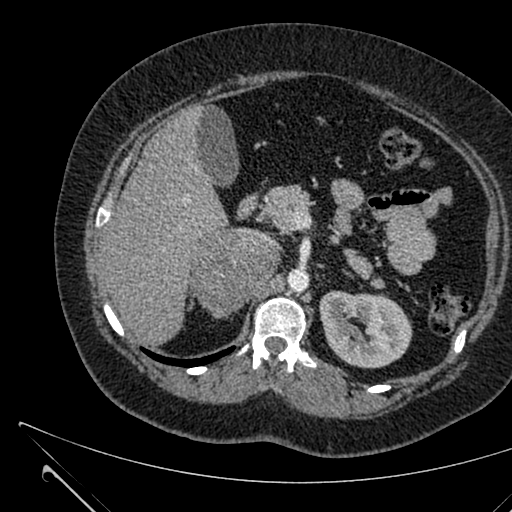
Contrast-enhanced abdominal CT, one axial slice; 120 kVp; intravenous contrast given; soft-tissue window (W 400 / L 40 HU); 1 mm slice thickness; 512 × 512 image matrix, field of view 376 × 376 mm. Patient: female, 36 years. Case-level facts recorded for this patient, not image findings: diagnosis: adrenocortical carcinoma; tumour side: right adrenal; tumour size at pathology: 10 cm; Ki-67 index: 20 %; stage (as recorded): 4.
Annotated regions visible in this slice (semi-automatically segmented with operator editing):
- mass: bounding box (x1, y1, x2, y2) in pixels: (192, 232, 280, 316)